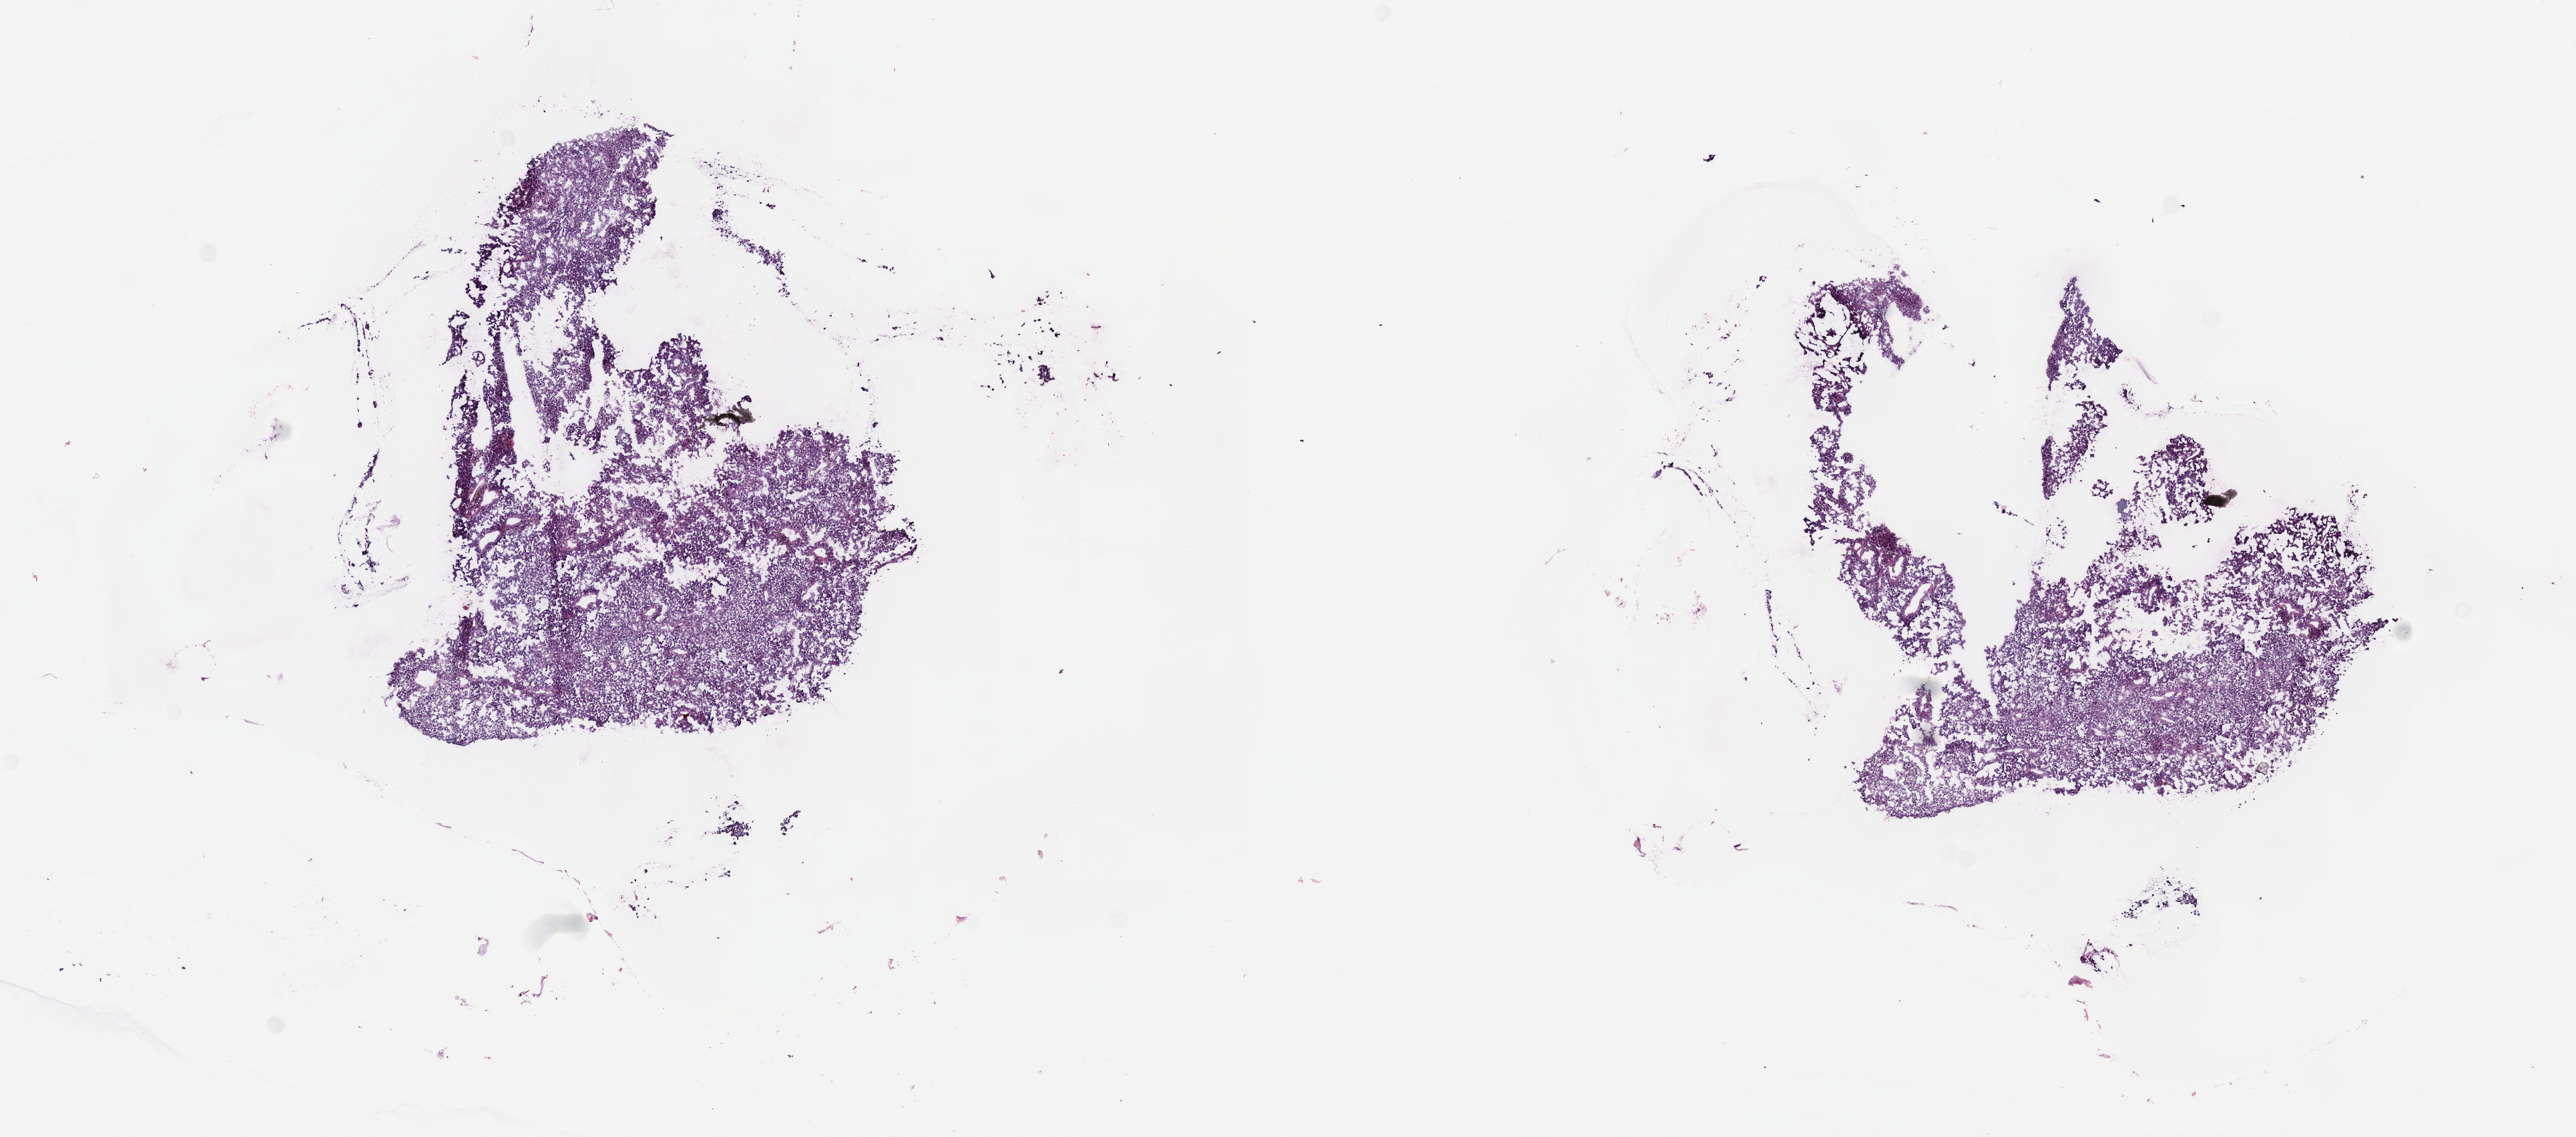
Whole-slide histology image, H&E, low-resolution overview of the scanned area, about 15.6 x 6.9 mm. Frozen section from the top of the tissue portion. Sample: primary tumour, uvea. Male, age 69 years at initial diagnosis.
Histologic diagnosis: Mixed epithelioid and spindle cell melanoma (overlapping lesion of eye and adnexa).